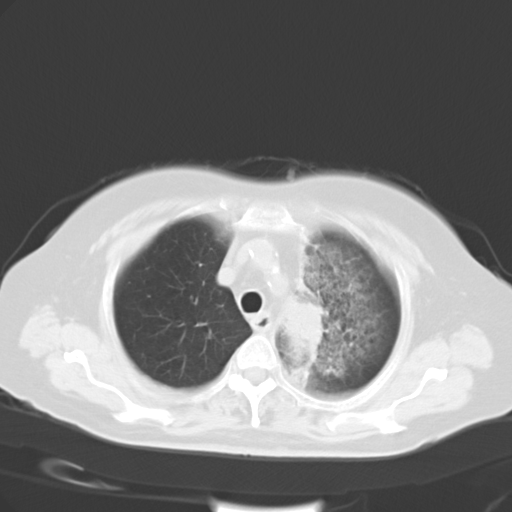
Chest CT, one axial slice. Position 22 of 27 along the scan axis. Reconstruction kernel B40f. Lung window (W 1500 / L -600 HU). 512 × 512 image matrix, field of view 353 × 353 mm. Female patient, age 65 years. Case-level facts recorded for this patient, not image findings: clinical TNM (as recorded): T2b N1 M0.
Outlined on this slice (rectangle marked by the reading radiologist):
- lung tumour (recorded histology: adenocarcinoma): bounding box <281,297,326,365> (left, top, right, bottom; pixels)